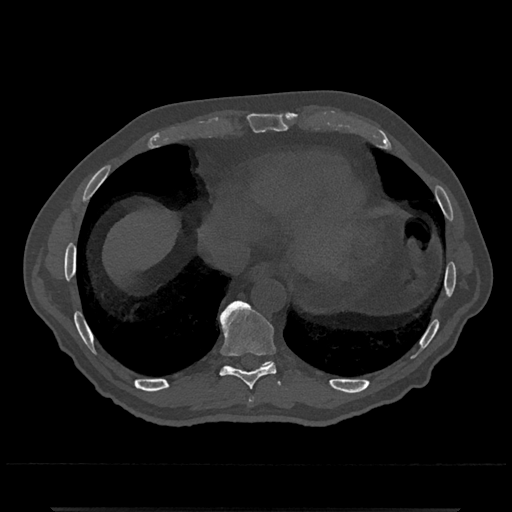
CT including the spine, one axial slice. Slice 603 of 797 in the series (ordered by position). 120 kVp. Bone window (W 1800 / L 400 HU). 0.5 mm slice thickness. 512 × 512 image matrix, field of view 393 × 393 mm. Male patient, age 67 years. Case-level facts recorded for this patient, not image findings: primary cancer: prostate.
Outlined on this slice (semi-automatic segmentation, software-assisted and operator-edited):
- T10 vertebra: bounding box (x1, y1, x2, y2) in pixels: (263, 361, 272, 366)
- T8 vertebra: (249, 398, 254, 402)
- T9 vertebra: (219, 300, 276, 390)